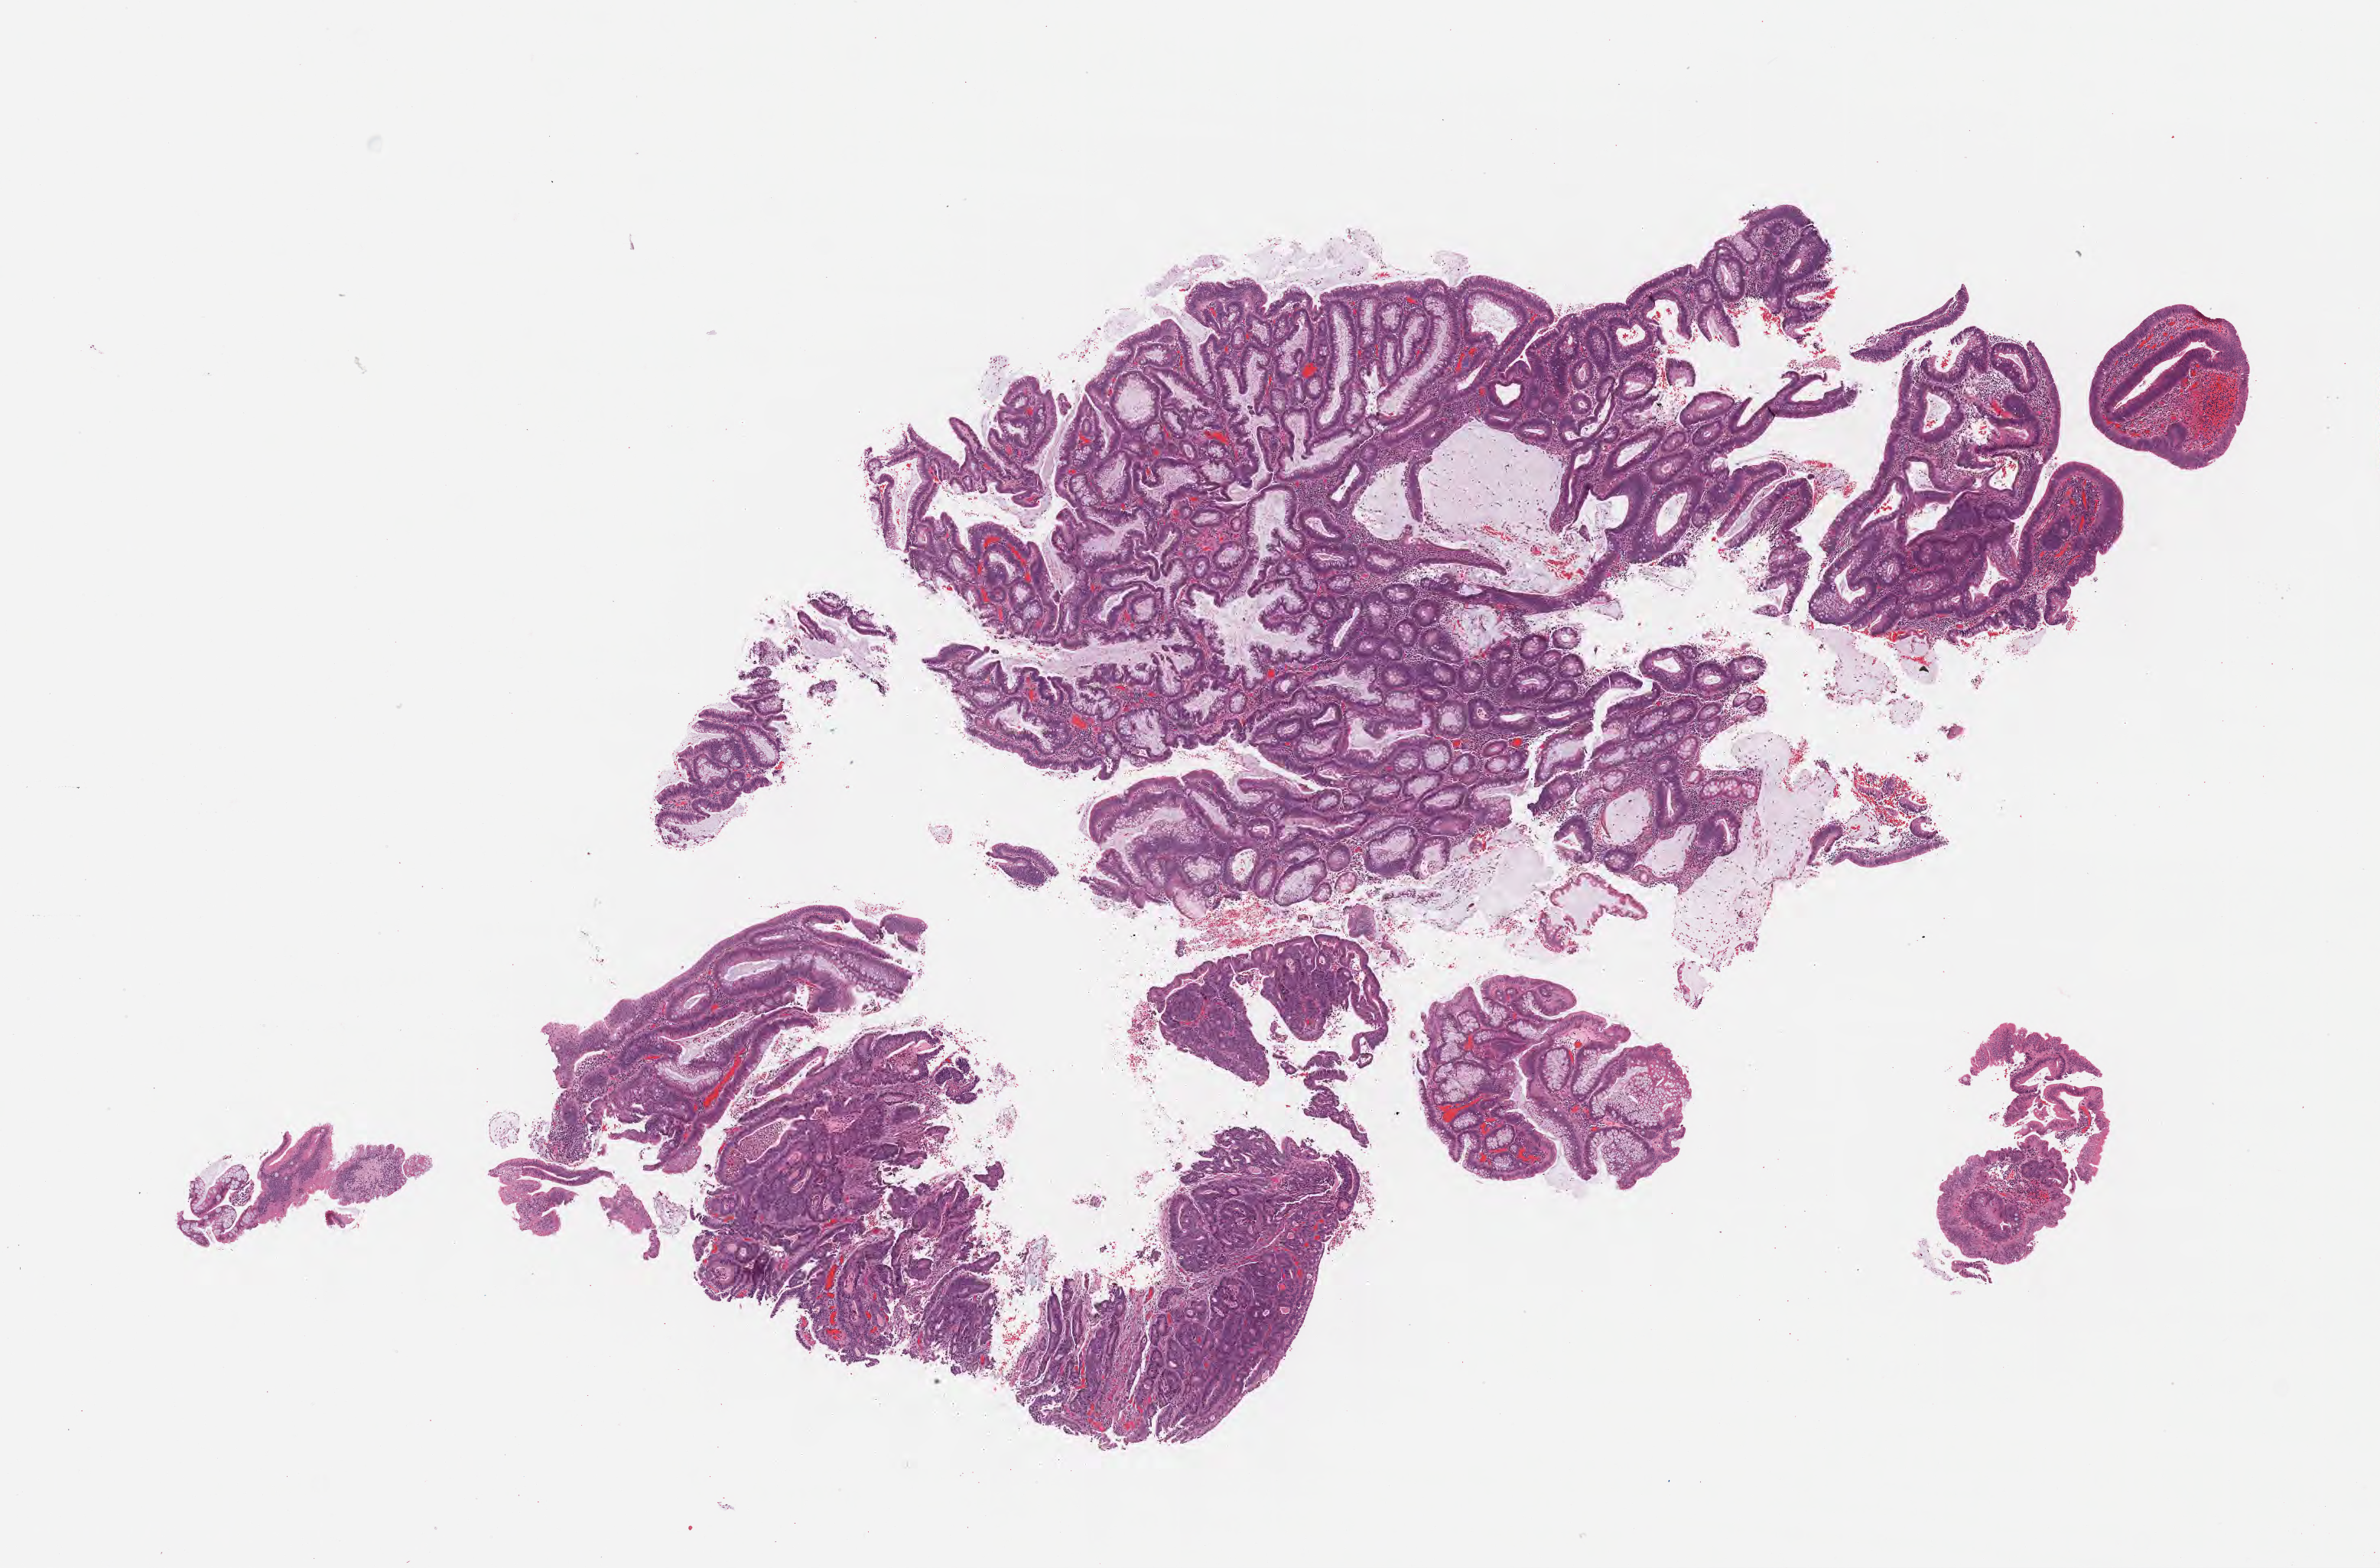
Haematoxylin and eosin whole-slide image — shown as a low-resolution overview of the whole scanned area (about 12.6 x 8.3 mm); FFPE section; specimen: primary tumor; anatomic site: cecum. Patient: male, age at initial diagnosis 75 years. Tumor grade: G2 (moderately differentiated). Slide review estimates, as recorded: tumor cells 20%, tumor nuclei 20%, stromal cells 20%, necrosis 0%, normal cells 60%. Inflammatory infiltration, as recorded: lymphocyte infiltration 0%, monocyte infiltration 0%, neutrophil infiltration 0%.
Histologic diagnosis: Adenocarcinoma, NOS. AJCC pathologic stage: Stage I.